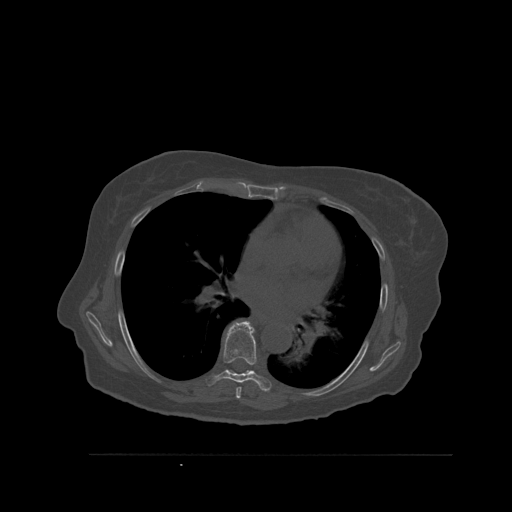
CT including the spine, one axial slice; slice 366 of 527 in the series (ordered by position); bone window (W 1800 / L 400 HU); 512 × 512 image matrix, field of view 470 × 470 mm. Patient: female, 73 years. Case-level facts recorded for this patient, not image findings: primary cancer: breast.
Annotated regions visible in this slice (semi-automatically segmented with operator editing):
- T6 vertebra: bounding box <236,387,242,399> (left, top, right, bottom; pixels)
- T7 vertebra: <206,321,272,392>